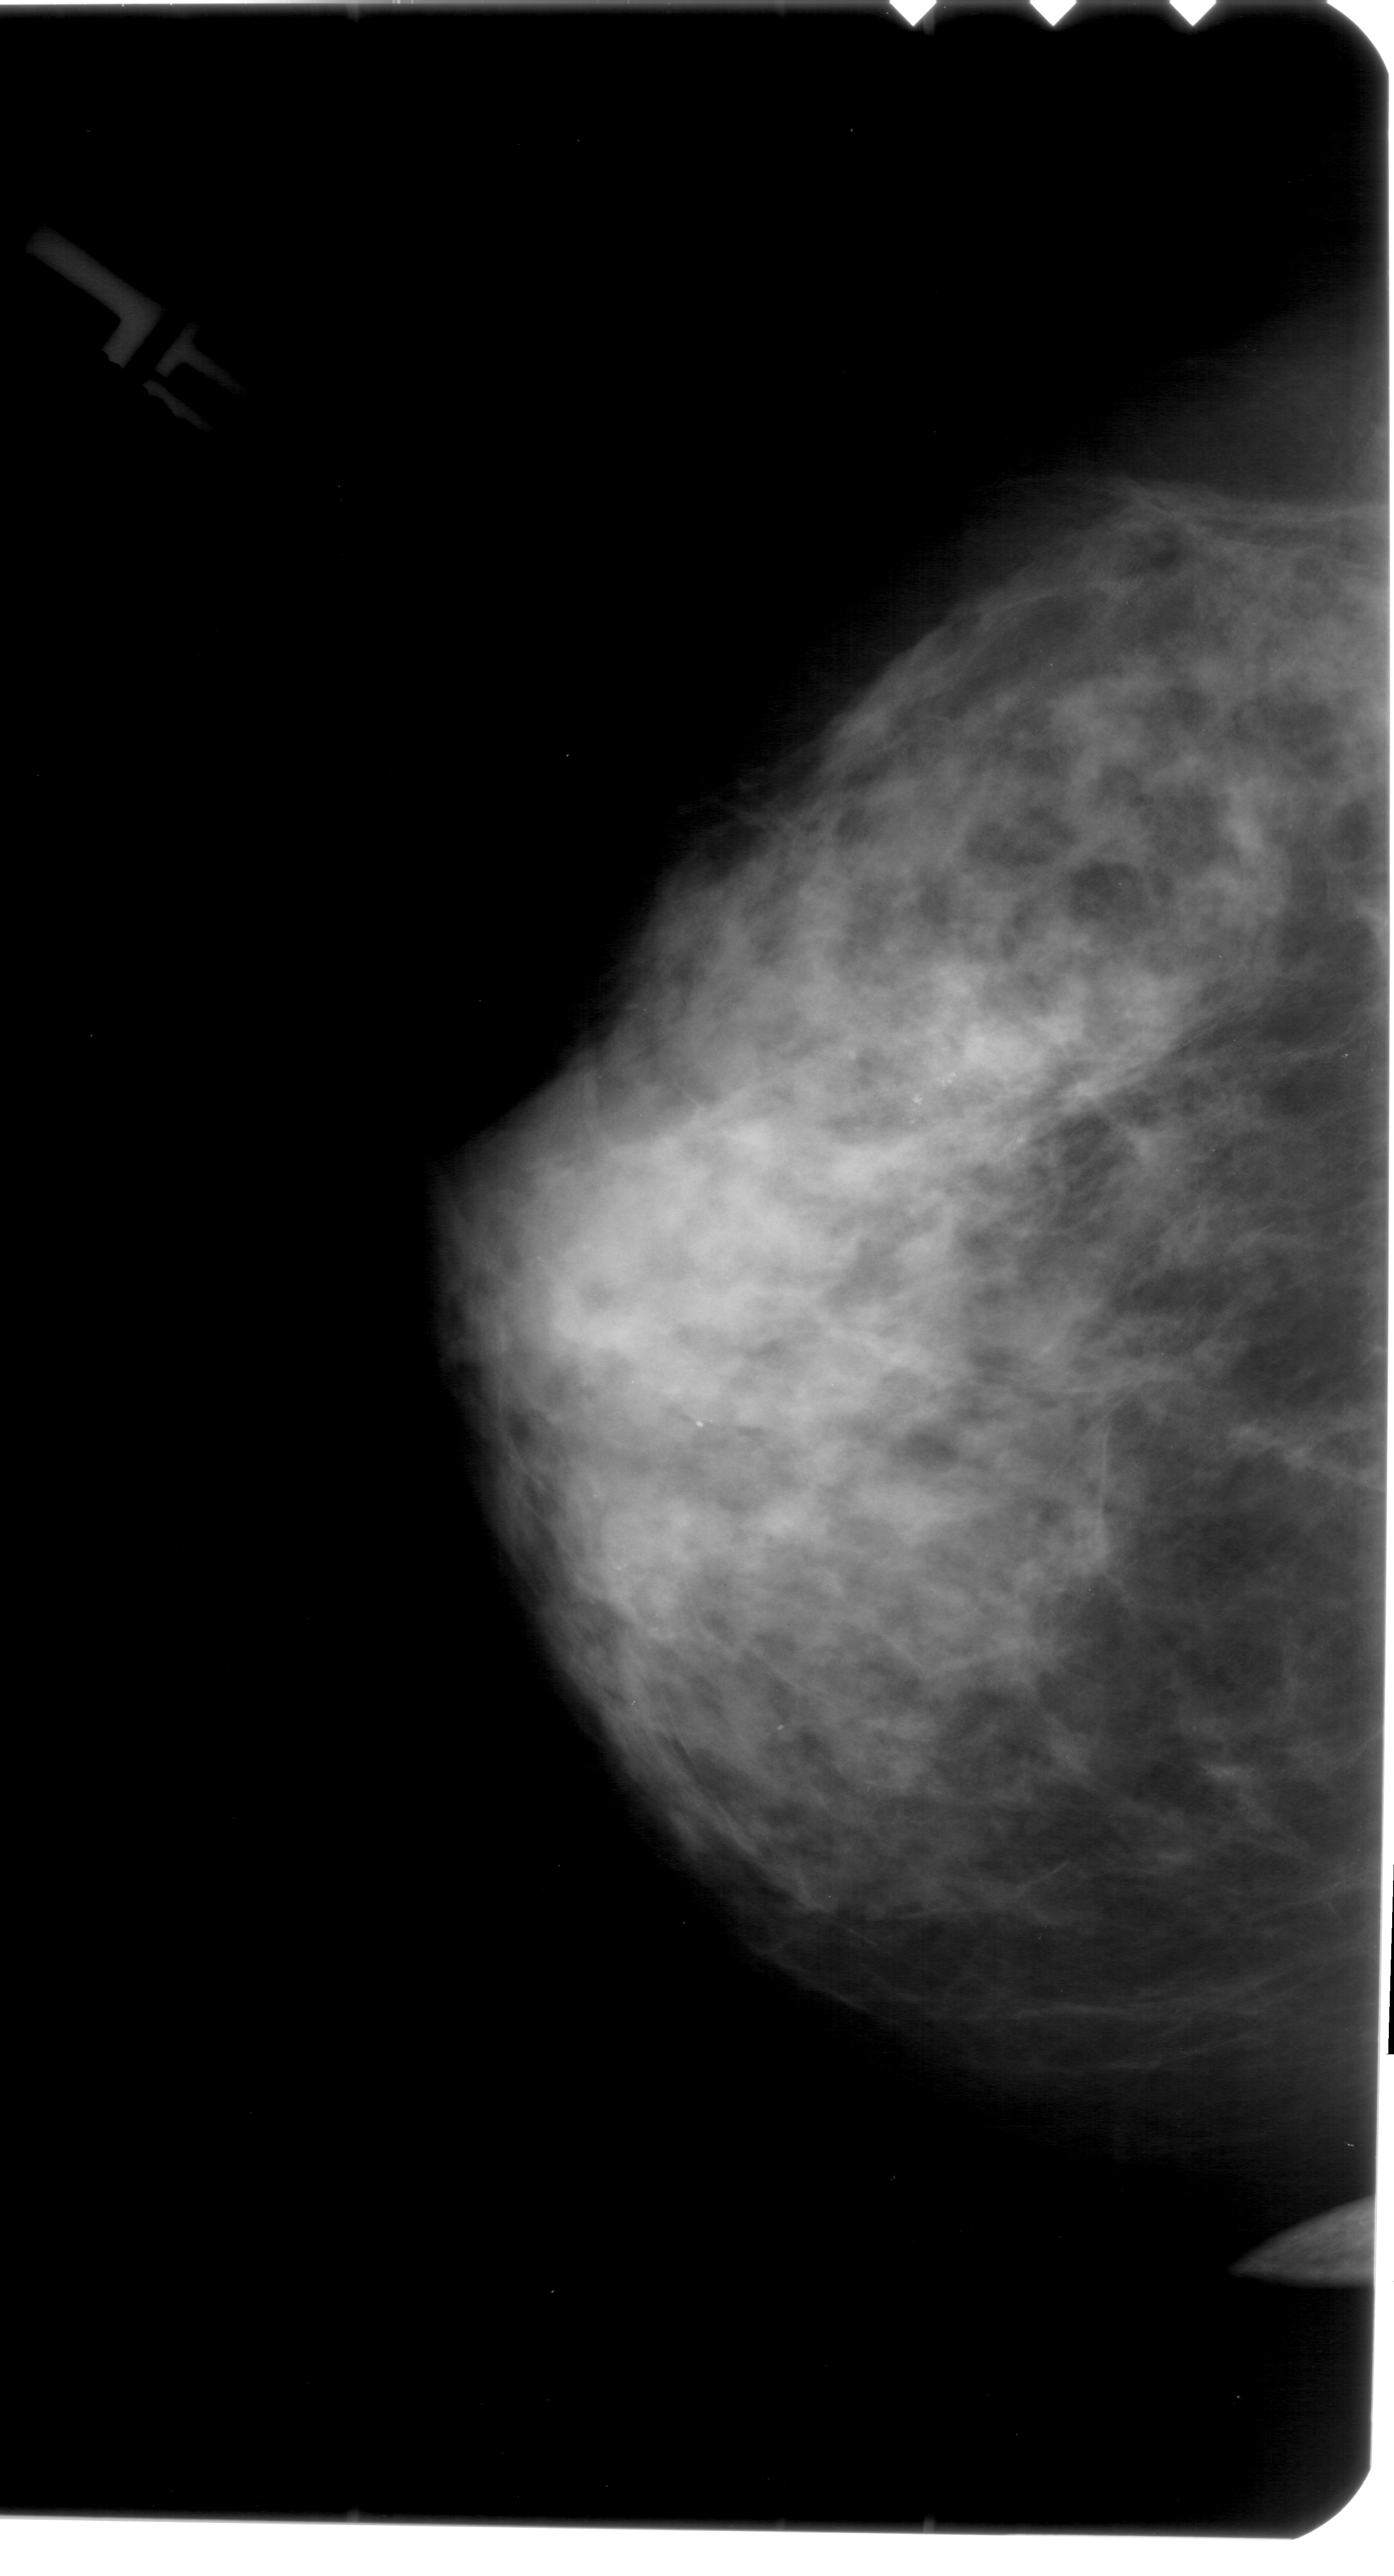
Digitized screen-film mammogram. Left breast. CC view. Breast composition: extremely dense (BI-RADS density category 4 of 4). 1394 × 2576 image matrix.
Expert-marked regions of interest on this film, with their recorded descriptors:
- calcifications, morphology pleomorphic, distribution clustered; BI-RADS assessment category 4; pathology (as recorded): malignant: box from (x=822, y=951) to (x=1004, y=1200) px